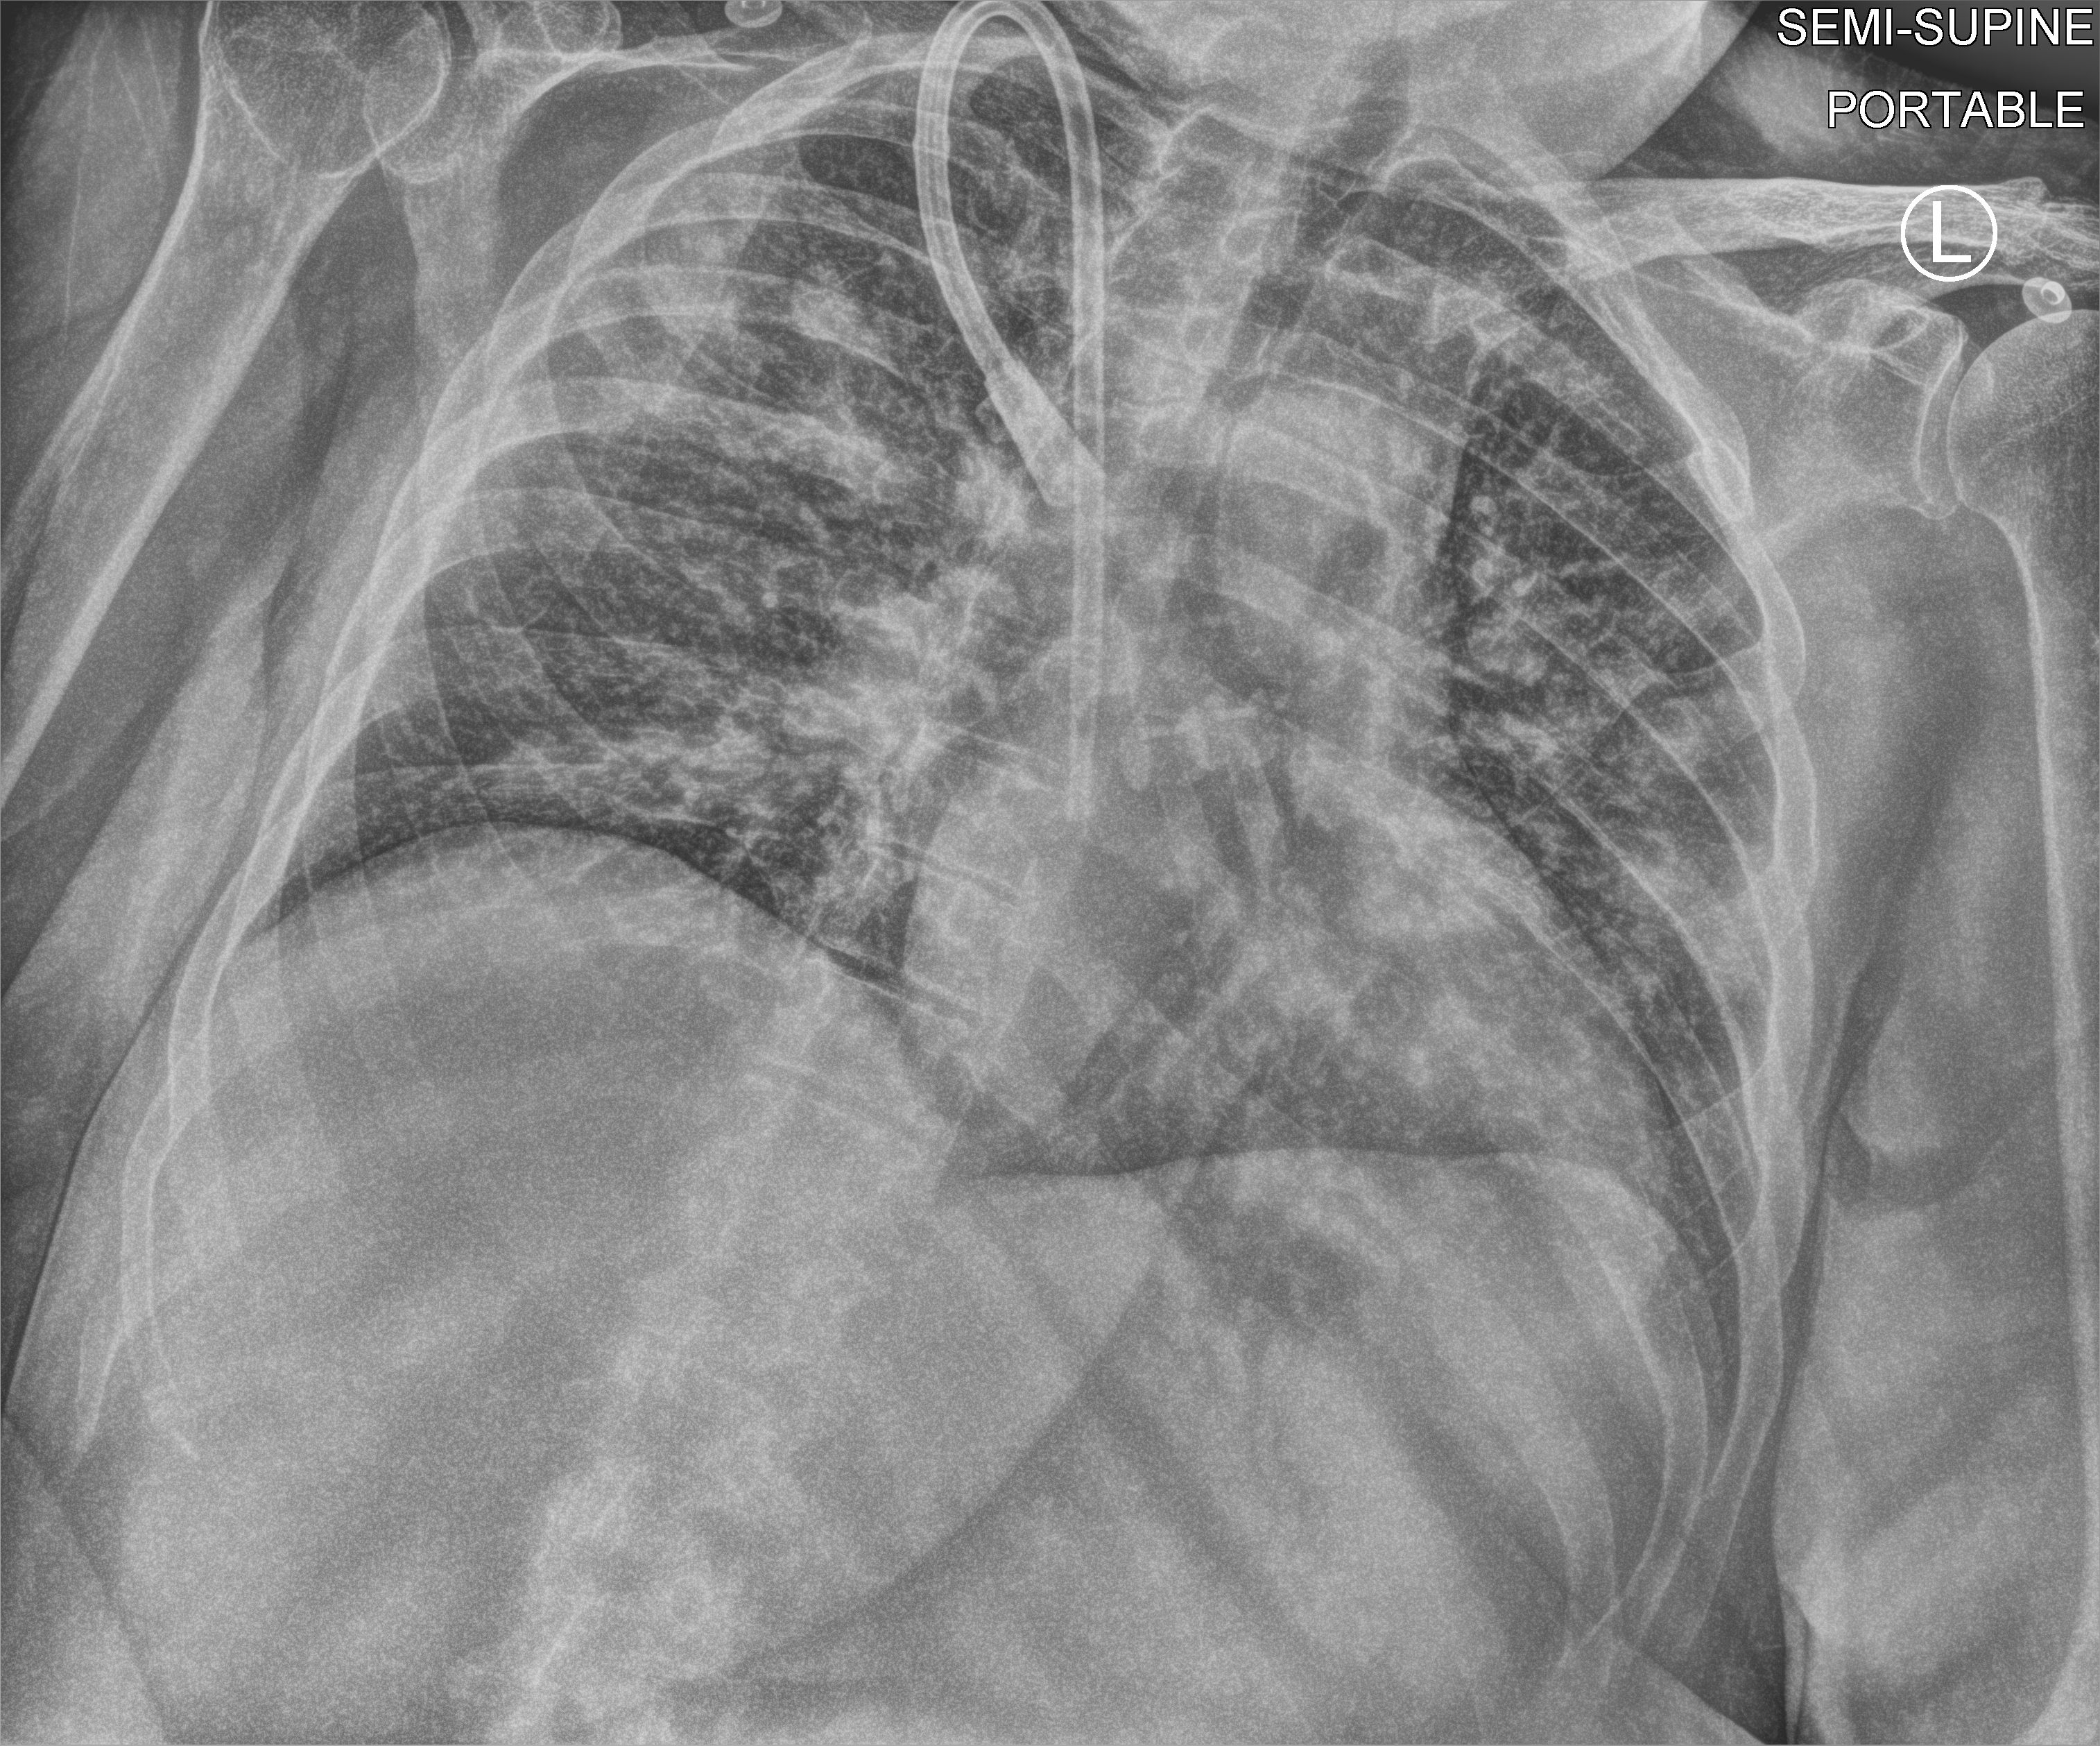
Bedside chest radiograph (computed radiography). Female patient hospitalised with COVID-19, age 60–74 years.
Admission-level facts for this patient (not findings on this image; timing relative to this image not recorded):
- admitted to intensive care during this hospital stay: no
- length of hospital stay: 8 days